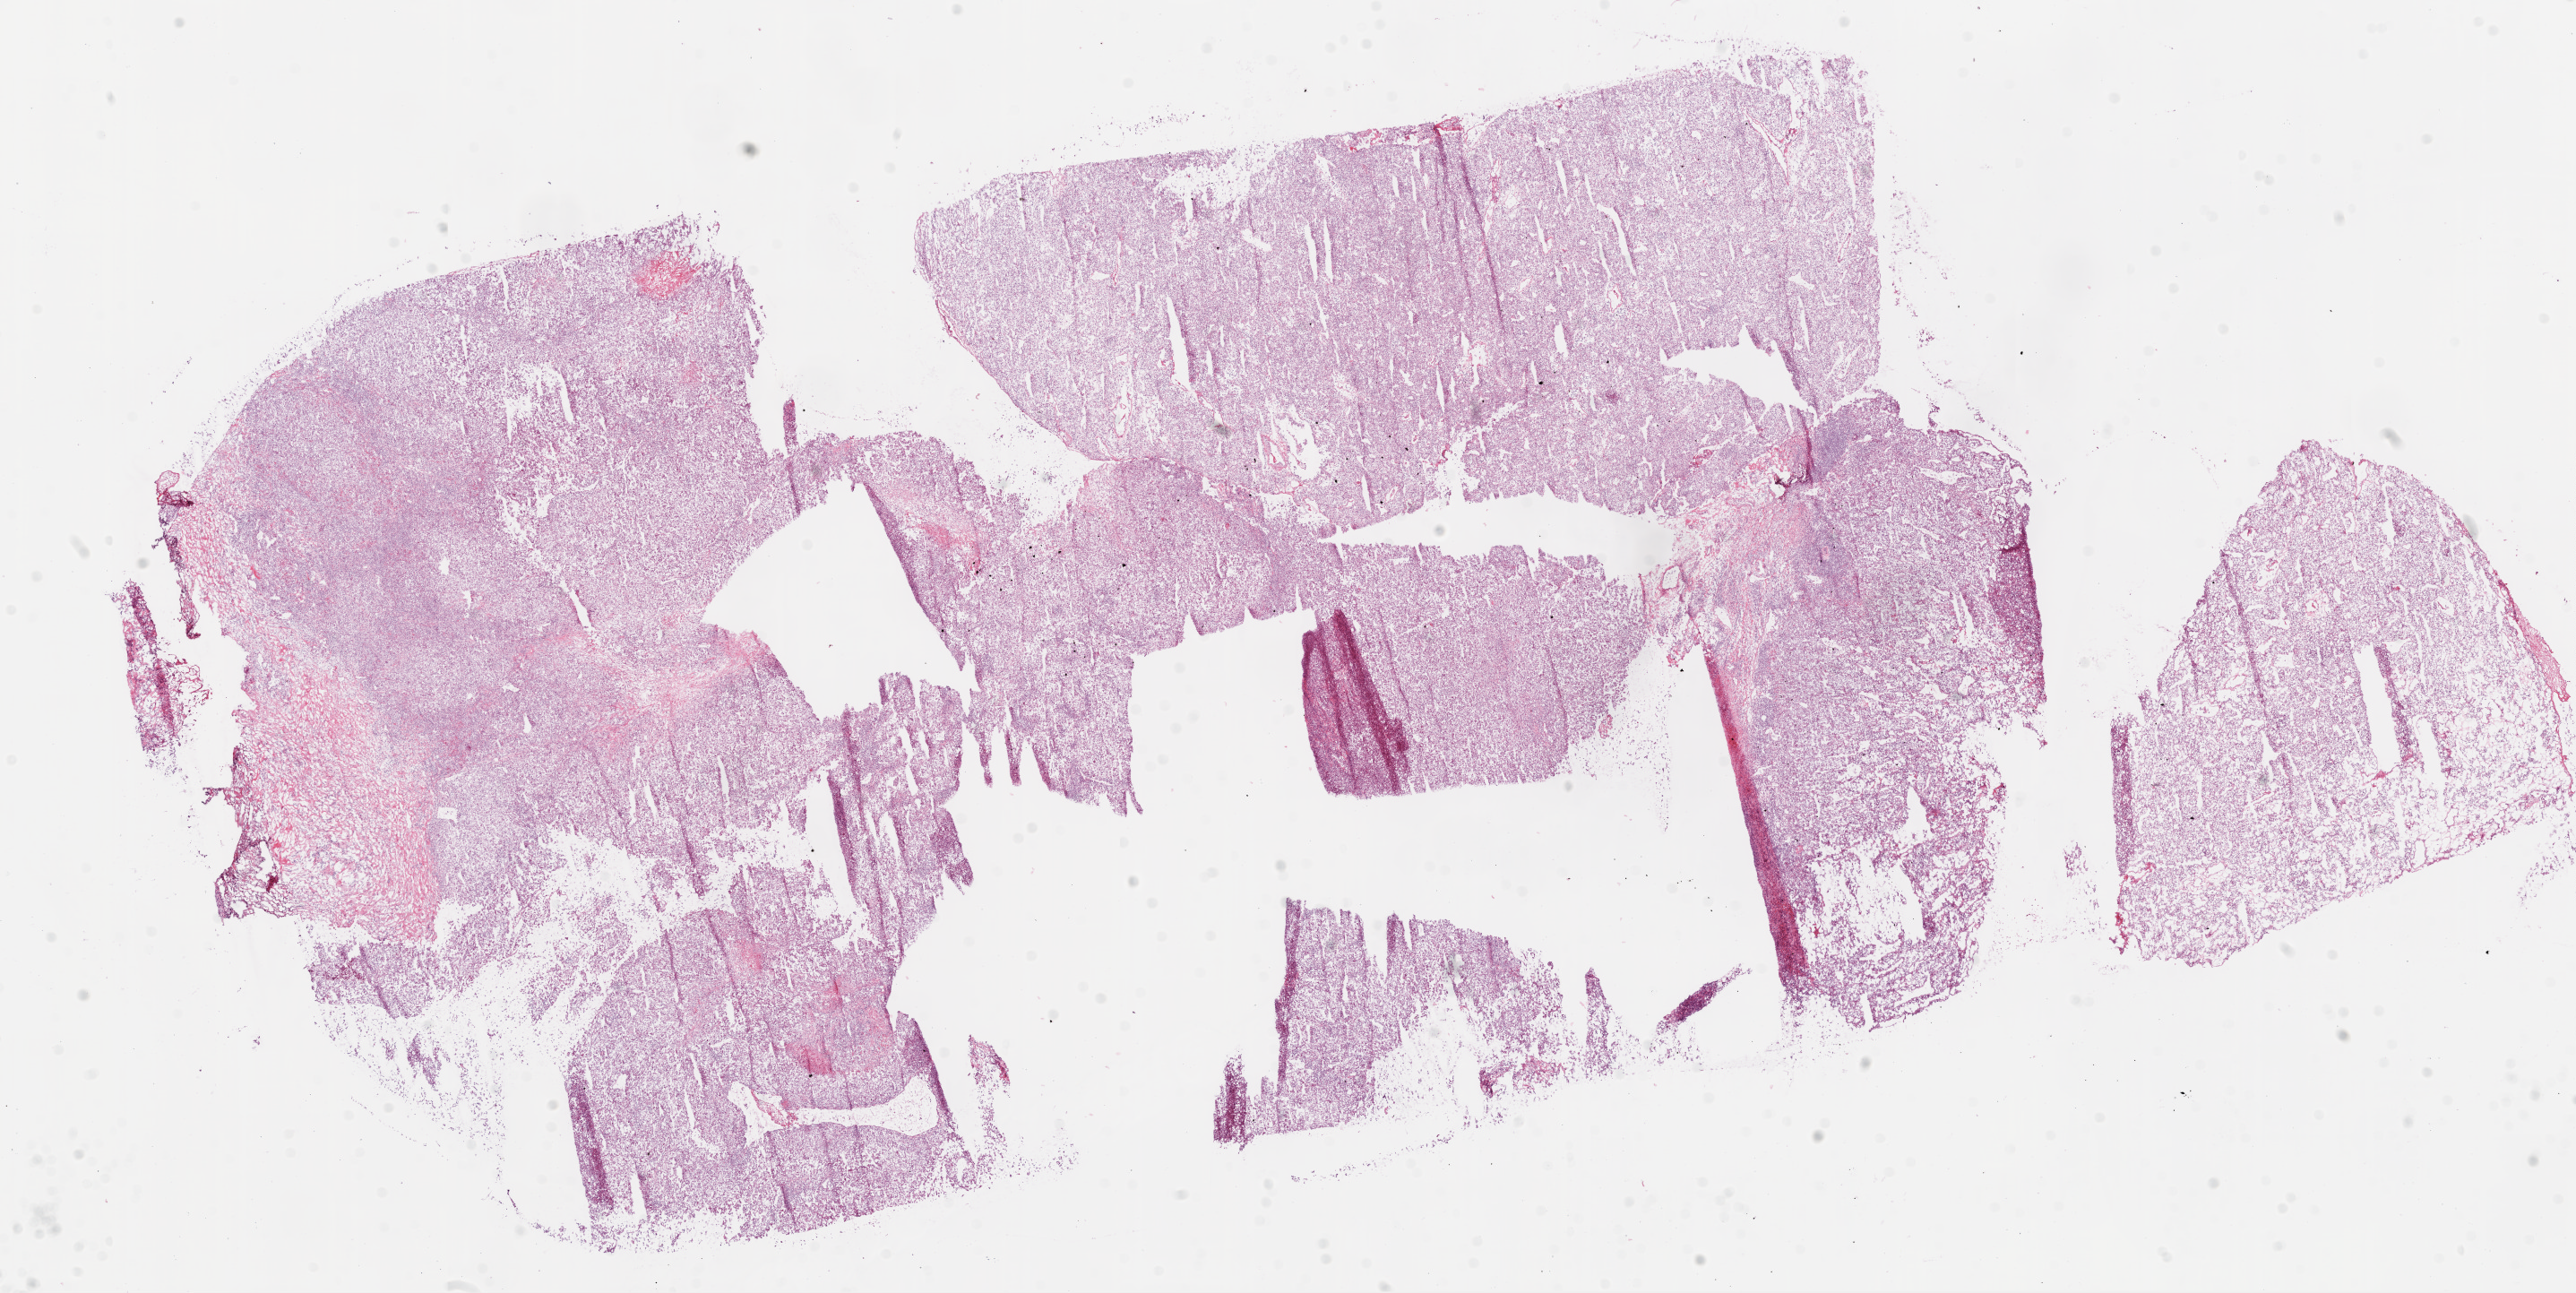
Whole-slide histology image, Hematoxylin and eosin (H&E) stained — shown as a low-resolution overview of the whole scanned area (about 23.1 x 11.6 mm), frozen section from the bottom of the tissue portion, primary tumour sample from the kidney. Female patient; age at initial diagnosis 52 years. Pathologist review of this section (percent, as recorded): tumour cells 95%, tumour nuclei 85%.
Diagnosis: Clear cell adenocarcinoma, NOS.